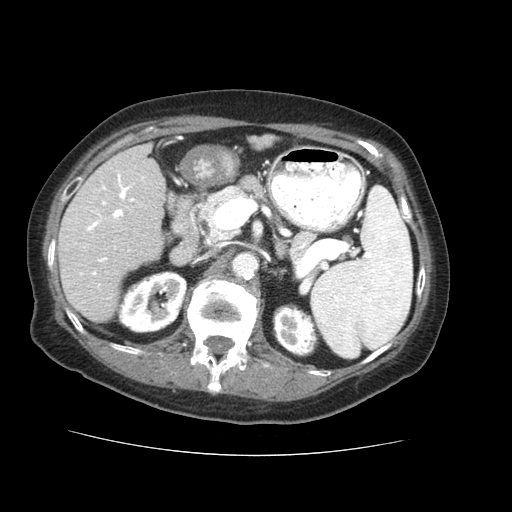
Contrast-enhanced abdominal CT (liver protocol), one axial slice; position 24 of 73 along the scan axis; reconstruction kernel STANDARD; soft-tissue window (W 400 / L 40 HU); 512 × 512 image matrix, field of view 360 × 360 mm. Case-level facts recorded for this patient, not image findings: diagnosis: hepatocellular carcinoma (patient treated with transarterial chemoembolisation; whether this scan precedes or follows treatment is not stated here); TNM stage (as recorded): Stage-IVB; Child-Pugh class: A; tumour differentiation: well differentiated.
Structures marked on this image (semi-automatically segmented with operator editing):
- liver parenchyma outside the tumour (the mass and vessels are separate outlines, so this box may not span the whole liver): bounding box <58,144,164,322> (left, top, right, bottom; pixels)
- liver vessels: <75,171,145,299>